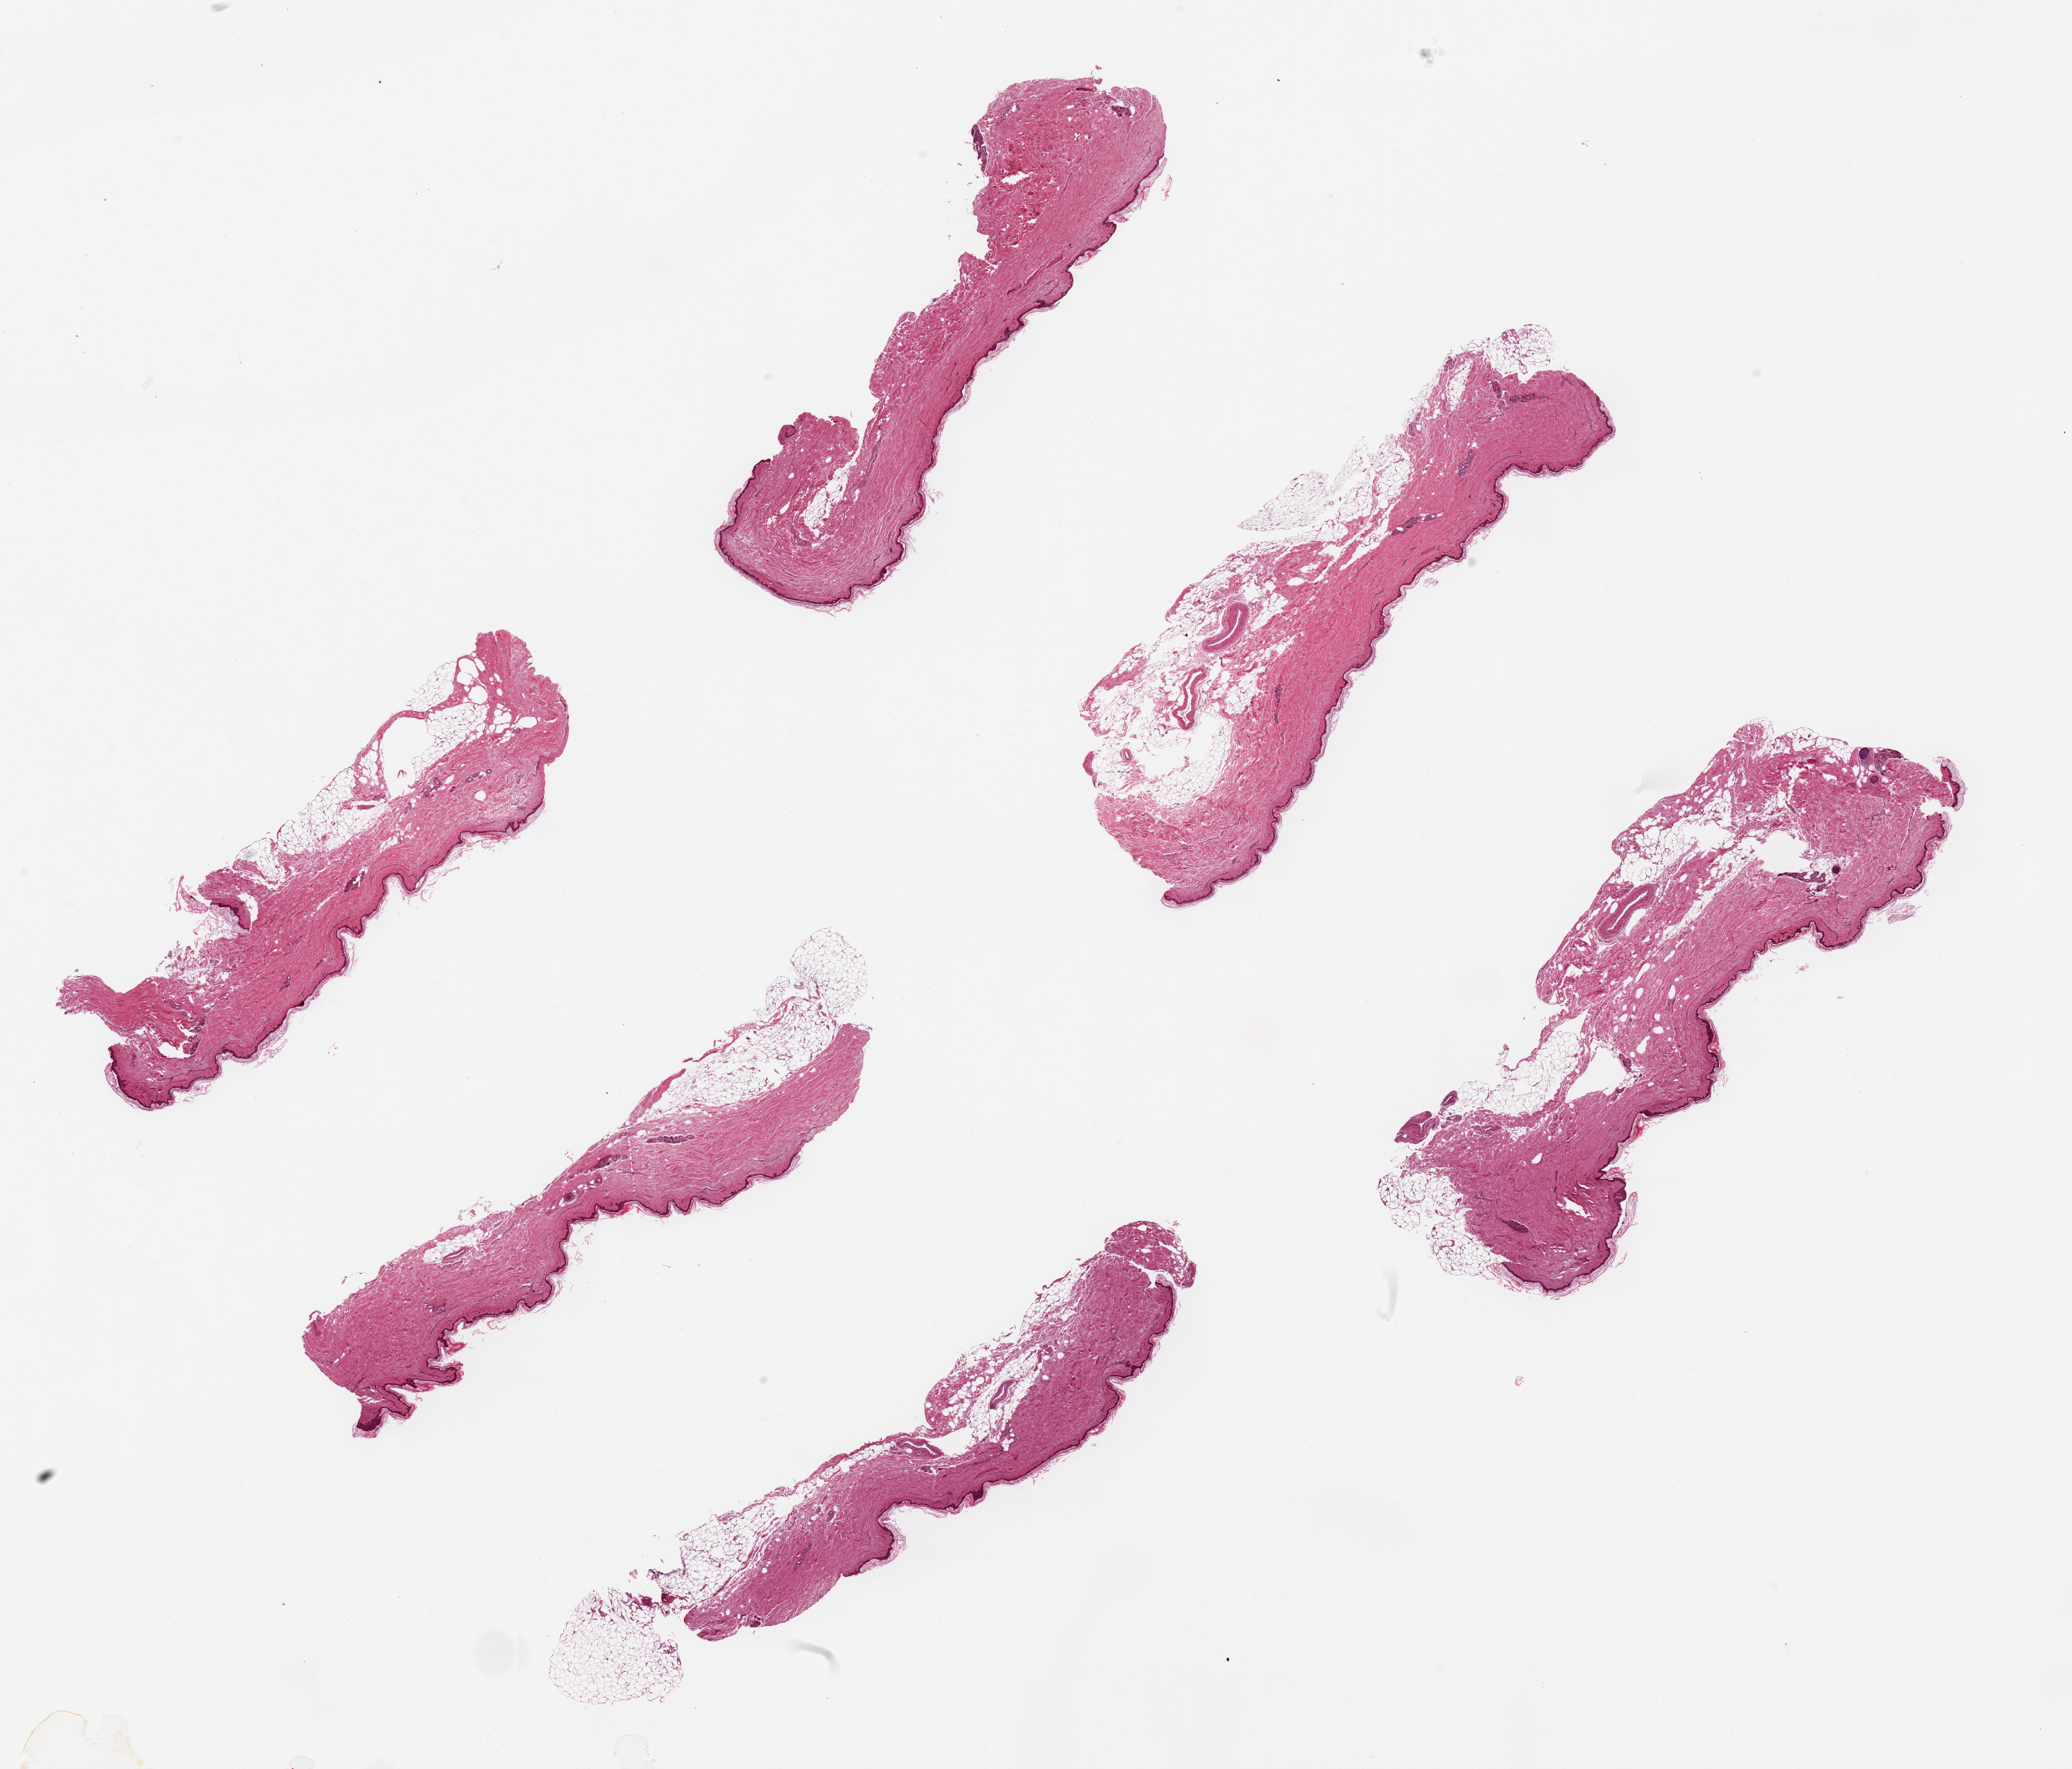
Whole-slide image, H&E stain — shown as a low-resolution overview of the whole scanned area (about 23.6 x 20.2 mm), PAXgene-fixed, paraffin-embedded tissue, sampled site (target tissue): skin of lower leg, tissue donor sample. Donor: female.
Pathologist's review note for this sample: 6 pieces, ~7x2mm. Squamous epithelium is ~1-2% of thickness.